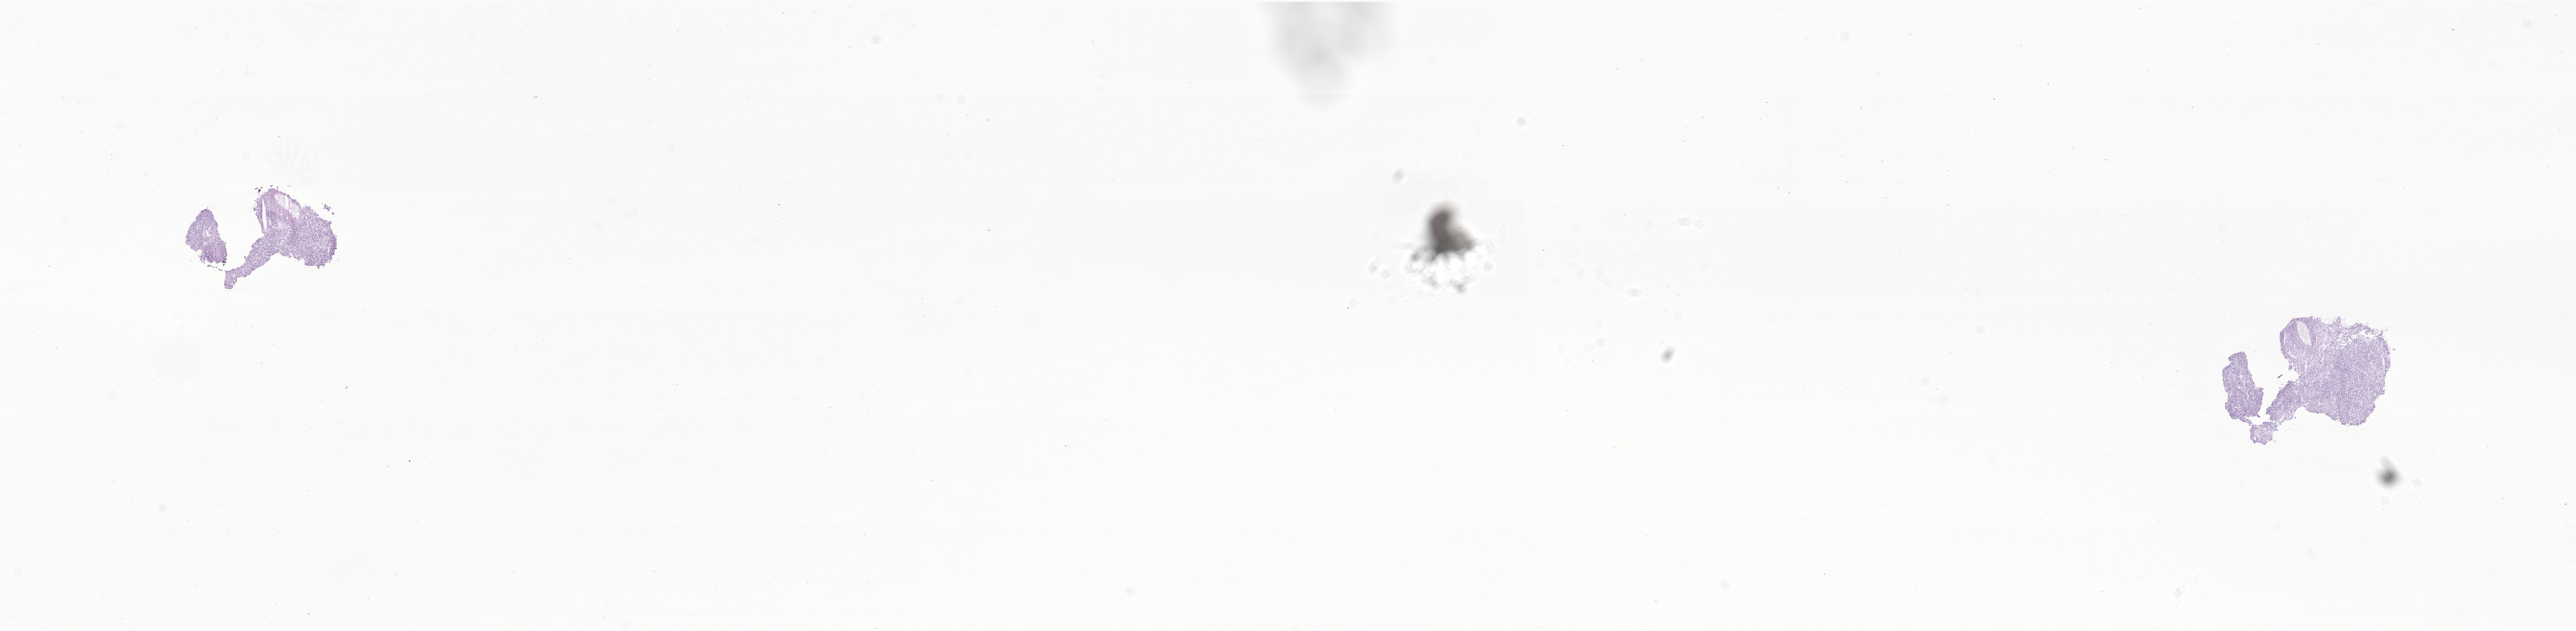
H&E whole-slide image of tumor tissue from the brain, a low-resolution overview of the entire scanned area, about 25.5 x 6.3 mm, frozen section (OCT-embedded). Patient: female, age 813 days (about 2.2 years).
Diagnosis (ICD-O-3 morphology term): Atypical teratoid/rhabdoid tumor.